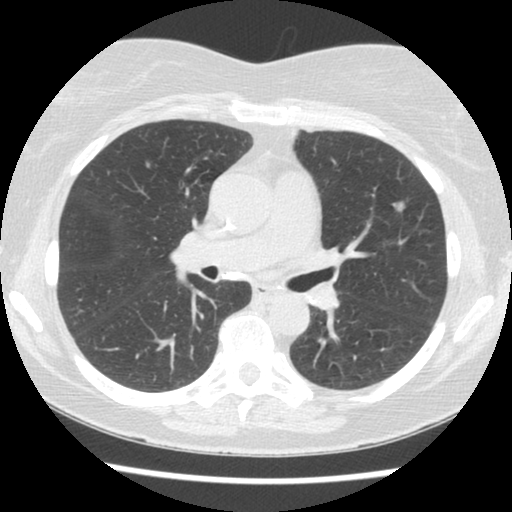
Low-dose screening chest CT, one axial slice; slice 68 of 120 in the series (ordered by position); 120 kVp; lung window (W 1500 / L -600 HU); 512 × 512 image matrix, field of view 310 × 310 mm.
Structures marked on this image (outlined manually by an expert reader):
- lesion 1 (tumor, upper lobe of left lung): box from (x=392, y=202) to (x=405, y=212) px